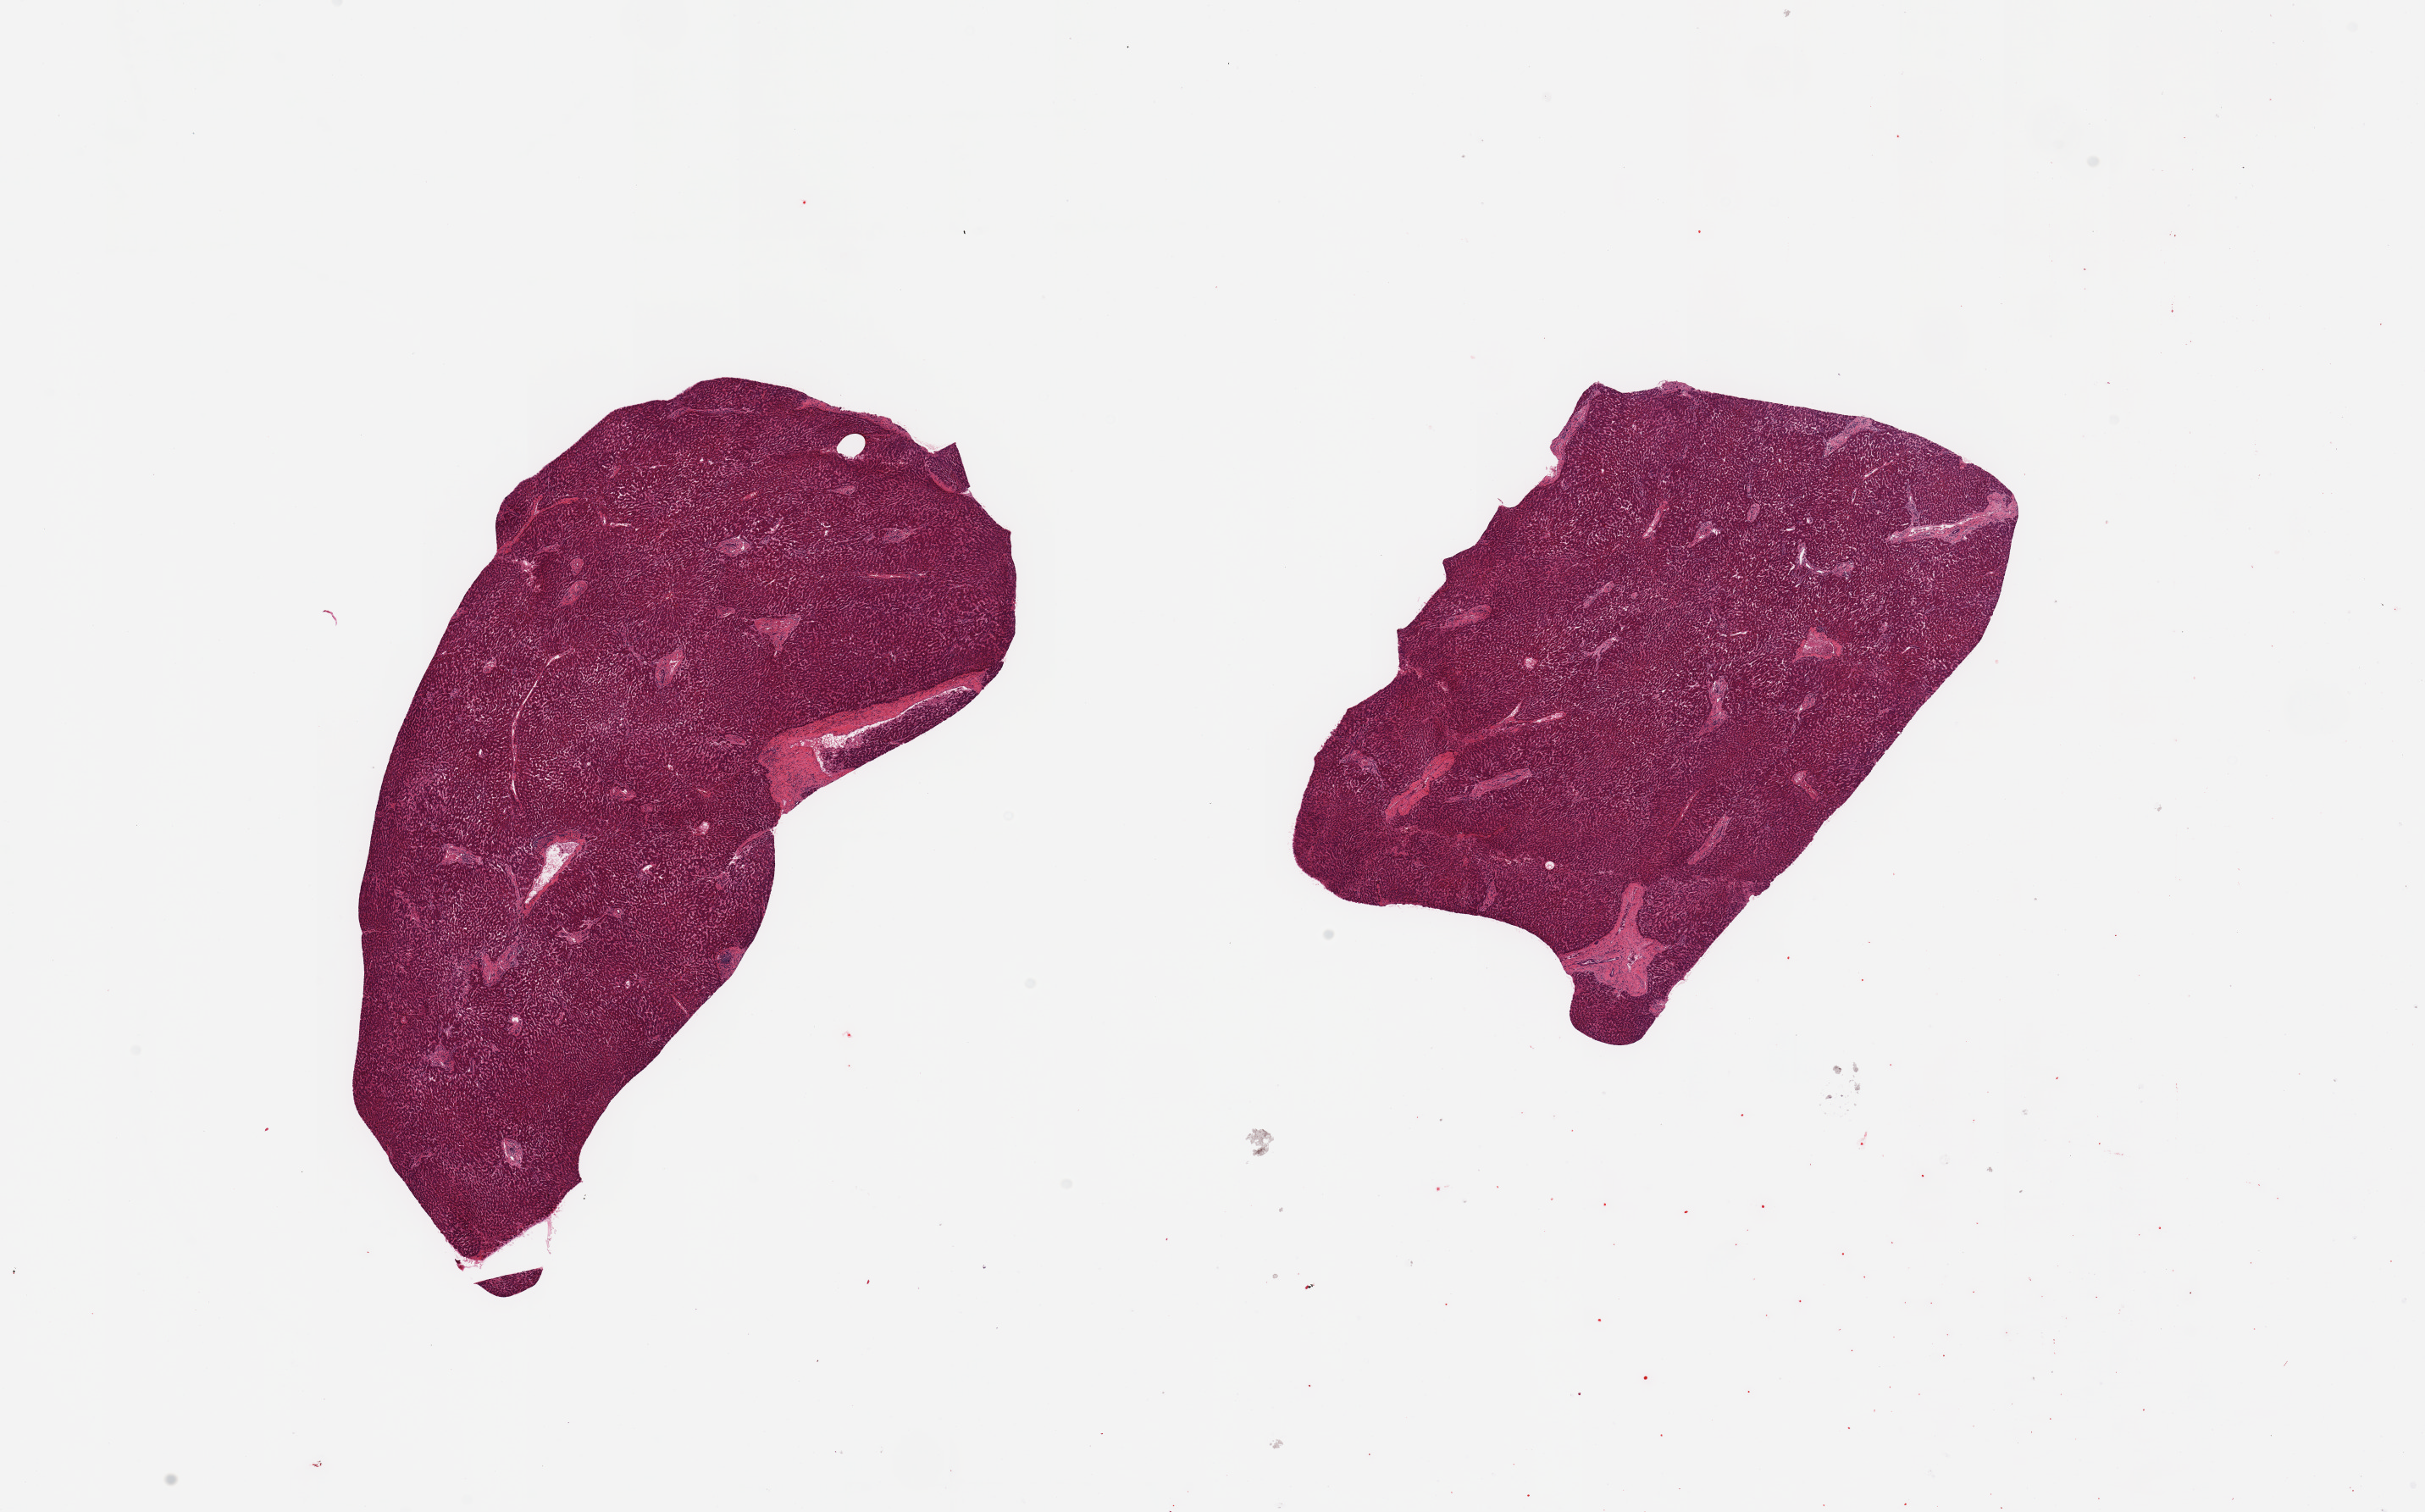
Haematoxylin and eosin whole-slide image — low-resolution overview of the scanned area, about 22.6 x 14.1 mm (acquisition: 20x scan), PAXgene-fixed, paraffin-embedded tissue, target tissue: liver, donor tissue sample. Donor: male.
Review note (as recorded): 2 pieces; mild microvesicular steatosis.